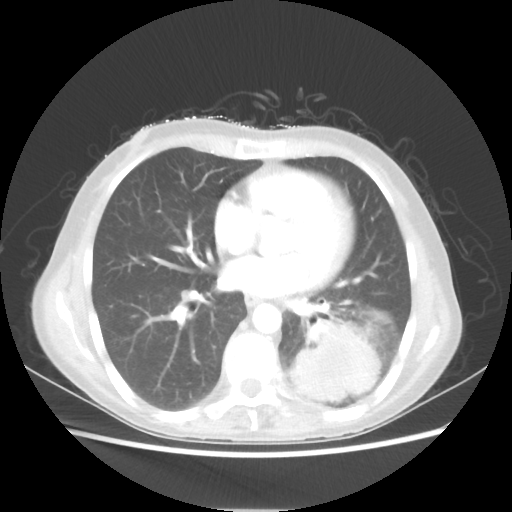
Chest CT, one axial slice. Lung window (W 1500 / L -600 HU). 5 mm slice thickness. 512 × 512 image matrix, field of view 360 × 360 mm. Patient: female, 53 years. Case-level facts recorded for this patient, not image findings: clinical TNM (as recorded): T3 N0 M0.
Structures marked on this image (rectangle marked by the reading radiologist):
- lung tumour (recorded histology: adenocarcinoma): bounding box <287,321,381,400> (left, top, right, bottom; pixels)